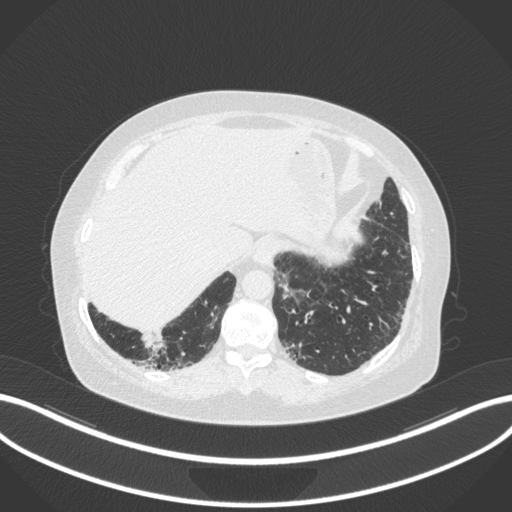
Chest CT, one axial slice. Position 15 of 303 along the scan axis. Reconstruction kernel B31f. 120 kVp. Lung window (W 1500 / L -600 HU). 1 mm slice thickness. 512 × 512 image matrix, field of view 400 × 400 mm. Patient: female, 65 years. Case-level facts recorded for this patient, not image findings: clinical TNM (as recorded): T2b N1 M0.
Outlined on this slice (bounding box drawn by a radiologist):
- lung tumour (recorded histology: adenocarcinoma): bounding box <137,333,168,356> (left, top, right, bottom; pixels)